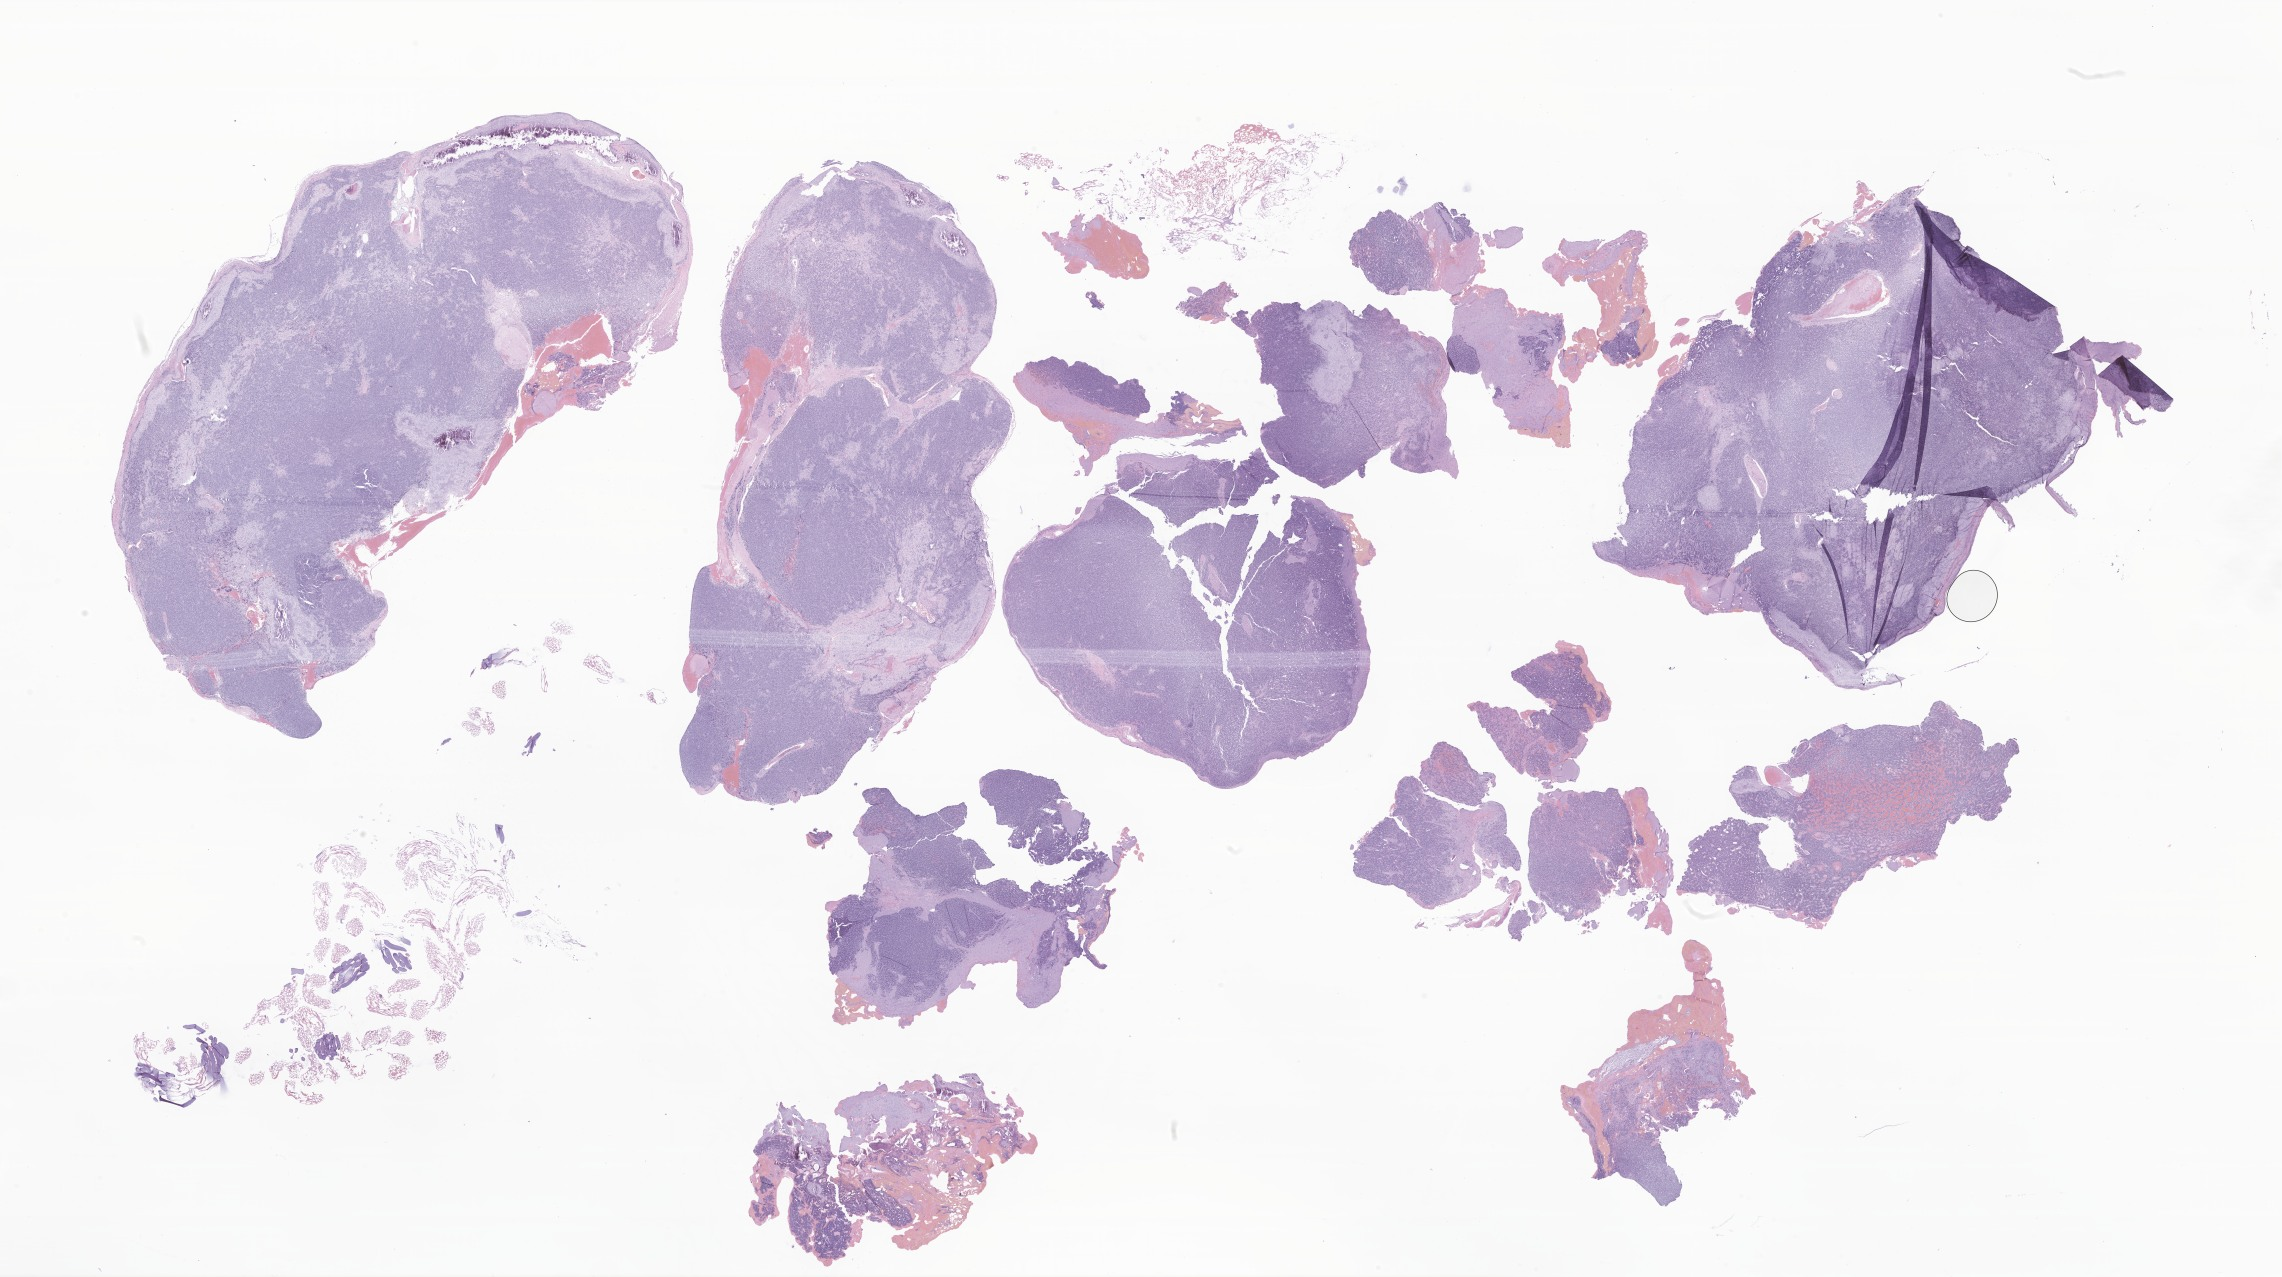
Haematoxylin and eosin whole-slide image of tumor tissue from the soft tissues of head and neck — whole scanned area (about 38.5 x 21.5 mm) shown as a low-resolution overview; formalin-fixed, paraffin-embedded (FFPE) tissue. Patient: male, age 177 months (14 years 9 months).
* recorded diagnosis: Mesenchymal chondrosarcoma